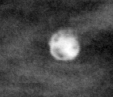
Cropped region of a digitized screen-film mammogram centred on a radiologist-marked abnormality; right breast; MLO view.
Finding: calcifications, morphology coarse / round and regular / lucent center; BI-RADS assessment category 2; subtlety rating 5 on a 1 (subtle) to 5 (obvious) scale; benign; no additional work-up was recommended (benign without callback).